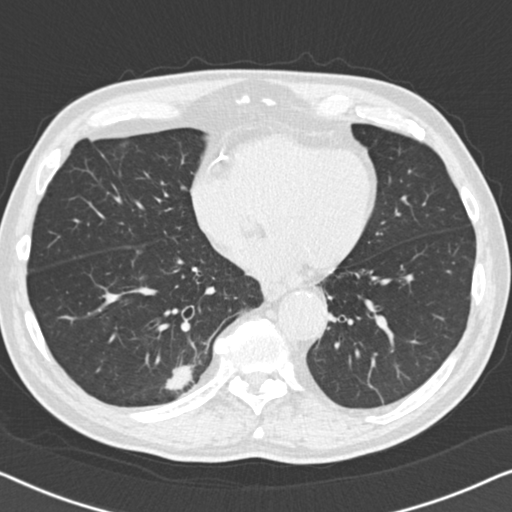
Low-dose screening chest CT, one axial slice; position 52 of 164 along the scan axis; reconstruction kernel B30f; 120 kVp; lung window (W 1500 / L -600 HU); 2 mm slice thickness; 512 × 512 image matrix.
Annotated regions visible in this slice (expert manual segmentation):
- lesion 1 (tumor, lower lobe of right lung): box from (x=164, y=364) to (x=194, y=391) px